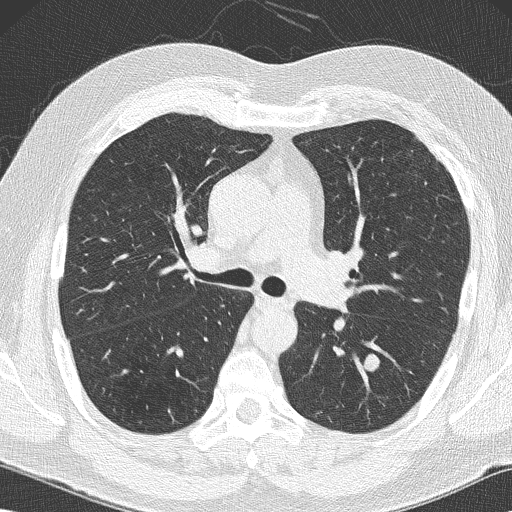
Low-dose screening chest CT, axial slice; first (baseline) screen; lung window (W 1500 / L -600 HU); slice 63 of 152 in the series. Male, age 59 years at enrolment.
Expert reader's lesion annotation, bounding box (x1, y1, x2, y2) in pixels: (345, 346, 389, 384). The screening reader recorded 2 non-calcified nodules or masses ≥4 mm on this exam (left lower lobe, left lower lobe); which of them this box marks is not recorded. Official screen result: positive, change unspecified: nodule(s) >= 4 mm or enlarging nodule(s), mass(es), or other non-specific abnormalities suspicious for lung cancer. Later outcome: lung cancer diagnosed 61 days after this screen — large cell carcinoma, NOS, left lower lobe, poorly differentiated (G3), stage IA (AJCC 6th edition), 14 mm at pathology.